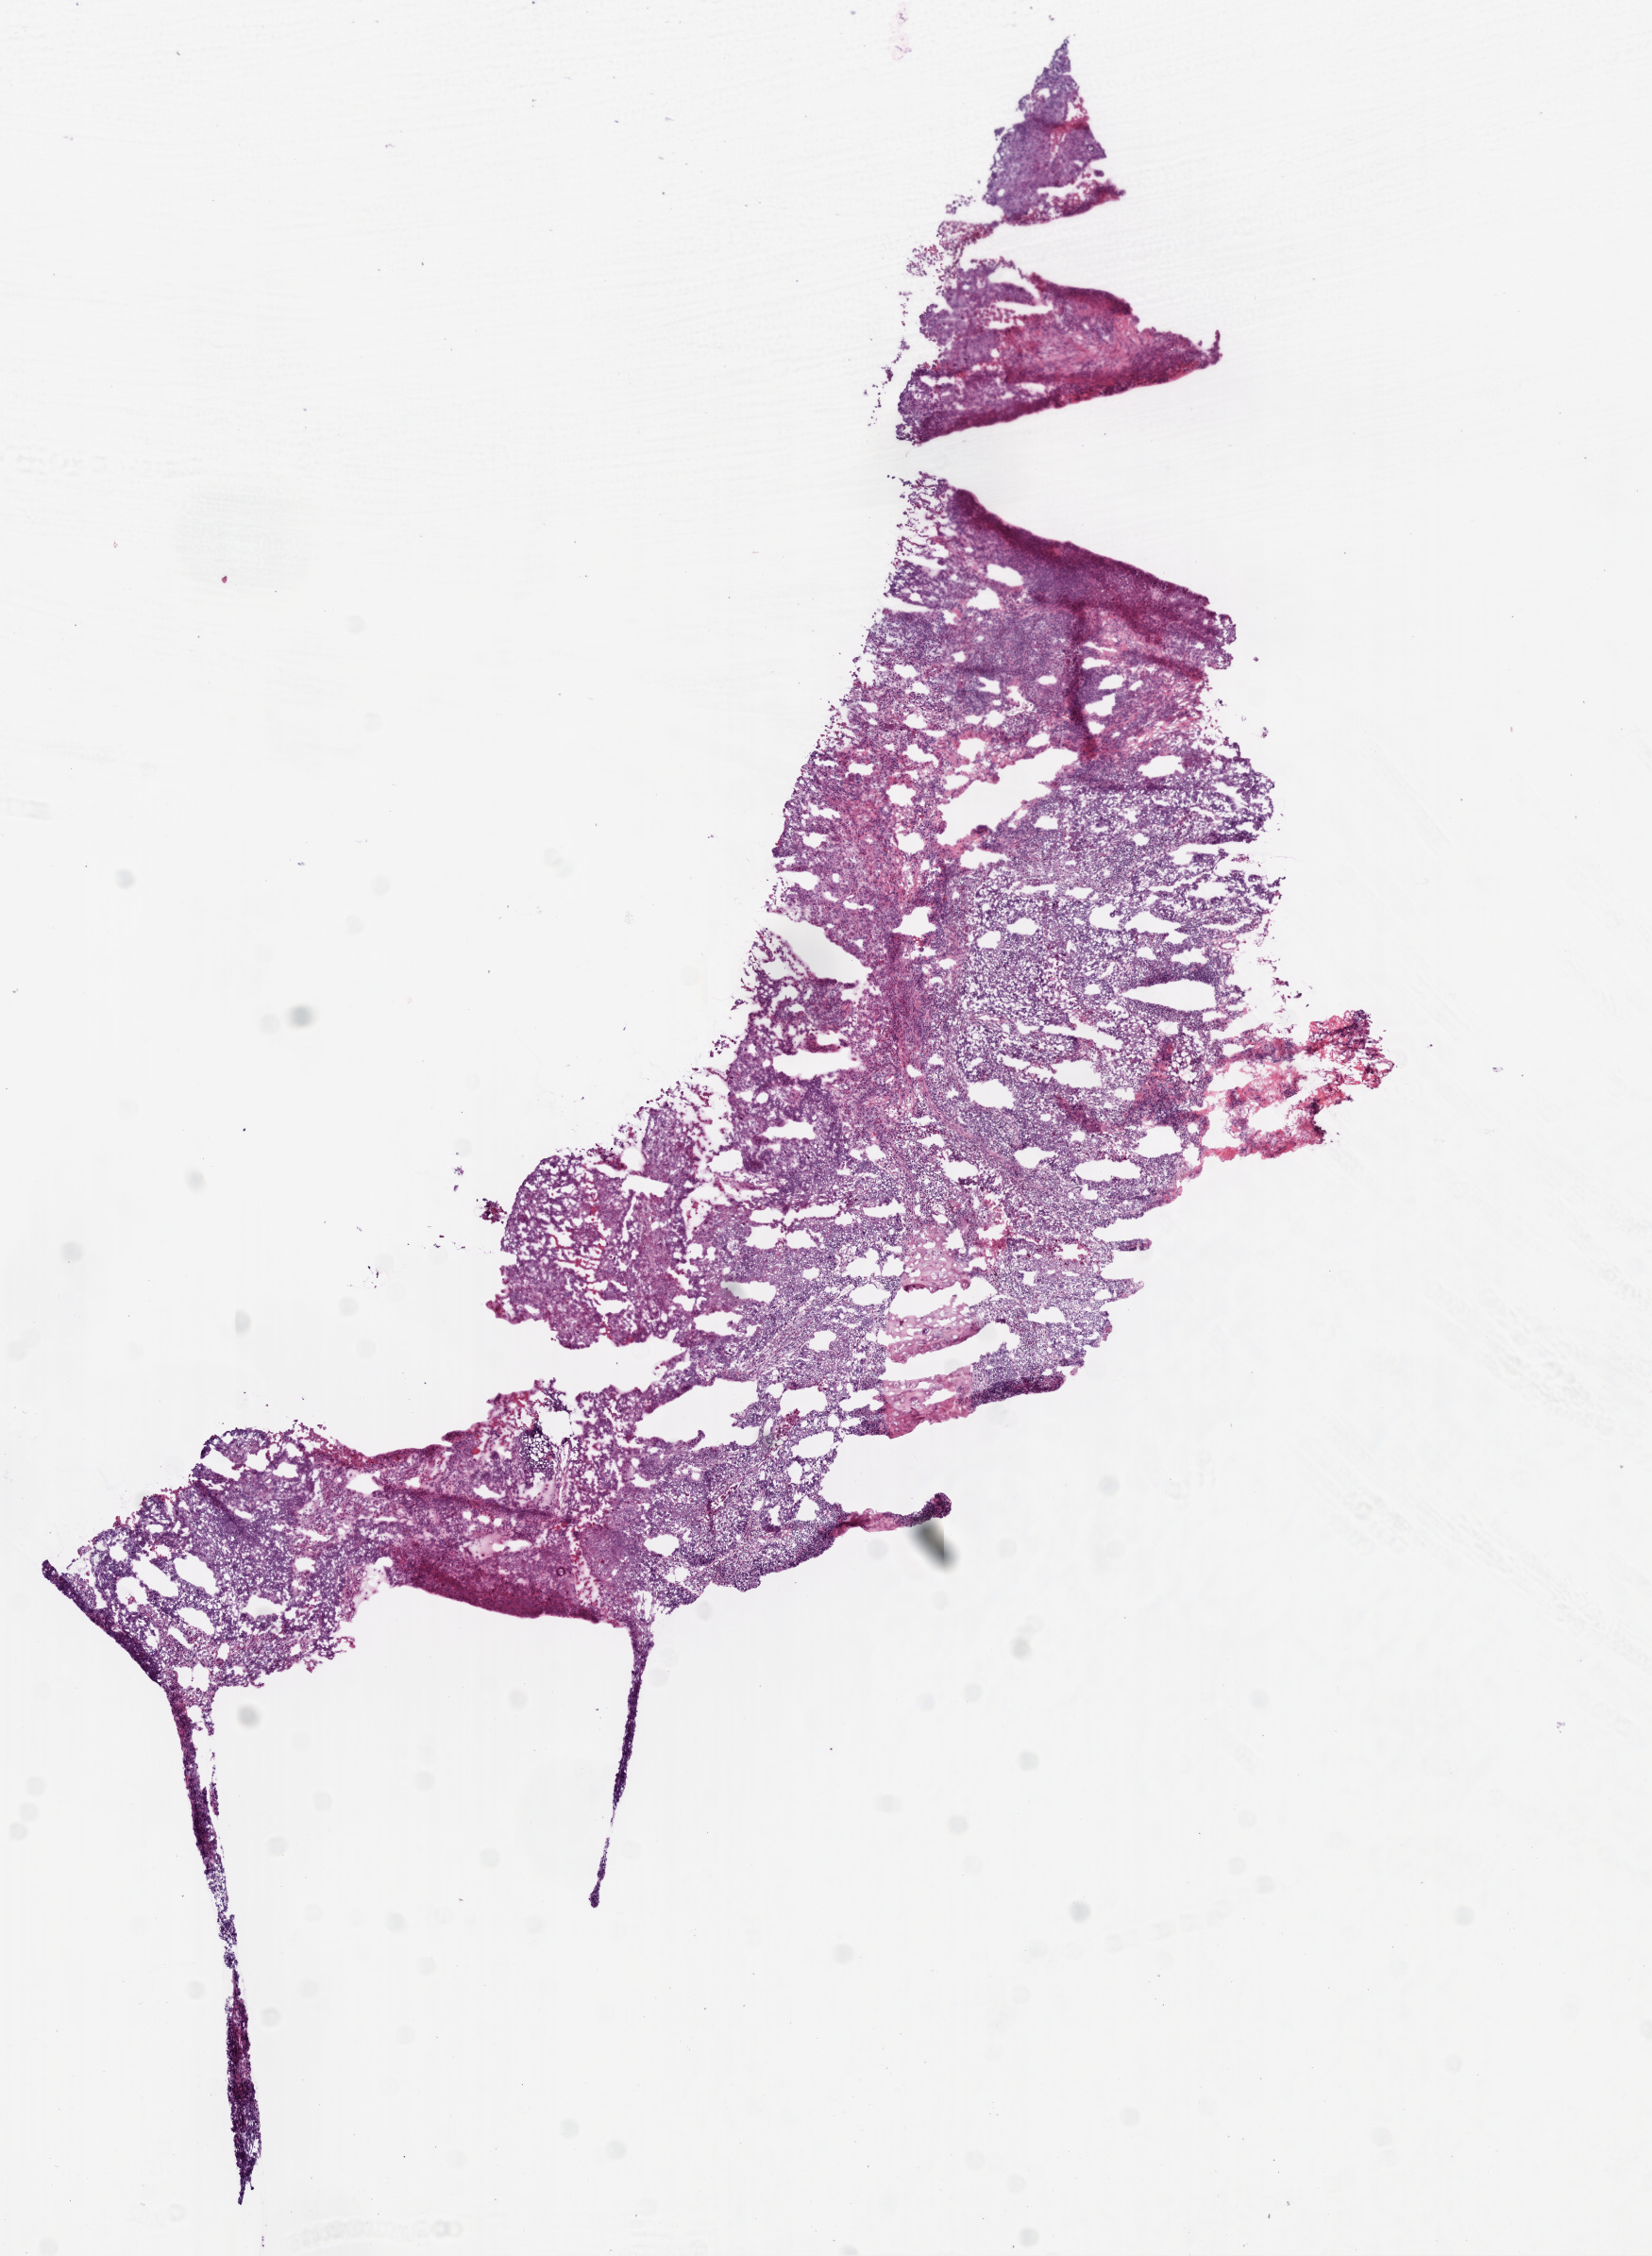
Hematoxylin and eosin (H&E) stained whole-slide image — shown as a low-resolution overview of the whole scanned area (about 7.0 x 9.6 mm). Frozen section from the bottom of the tissue portion. Primary tumour sample from the lung. Male patient; age at initial diagnosis 57 years. Composition of this section per pathologist review: tumour cells 93%, tumour nuclei 75%, normal cells 0%, stromal cells 5%, necrosis 2%.
• AJCC pathologic stage: IA (6th edition)
• pathologic diagnosis: Squamous cell carcinoma, NOS